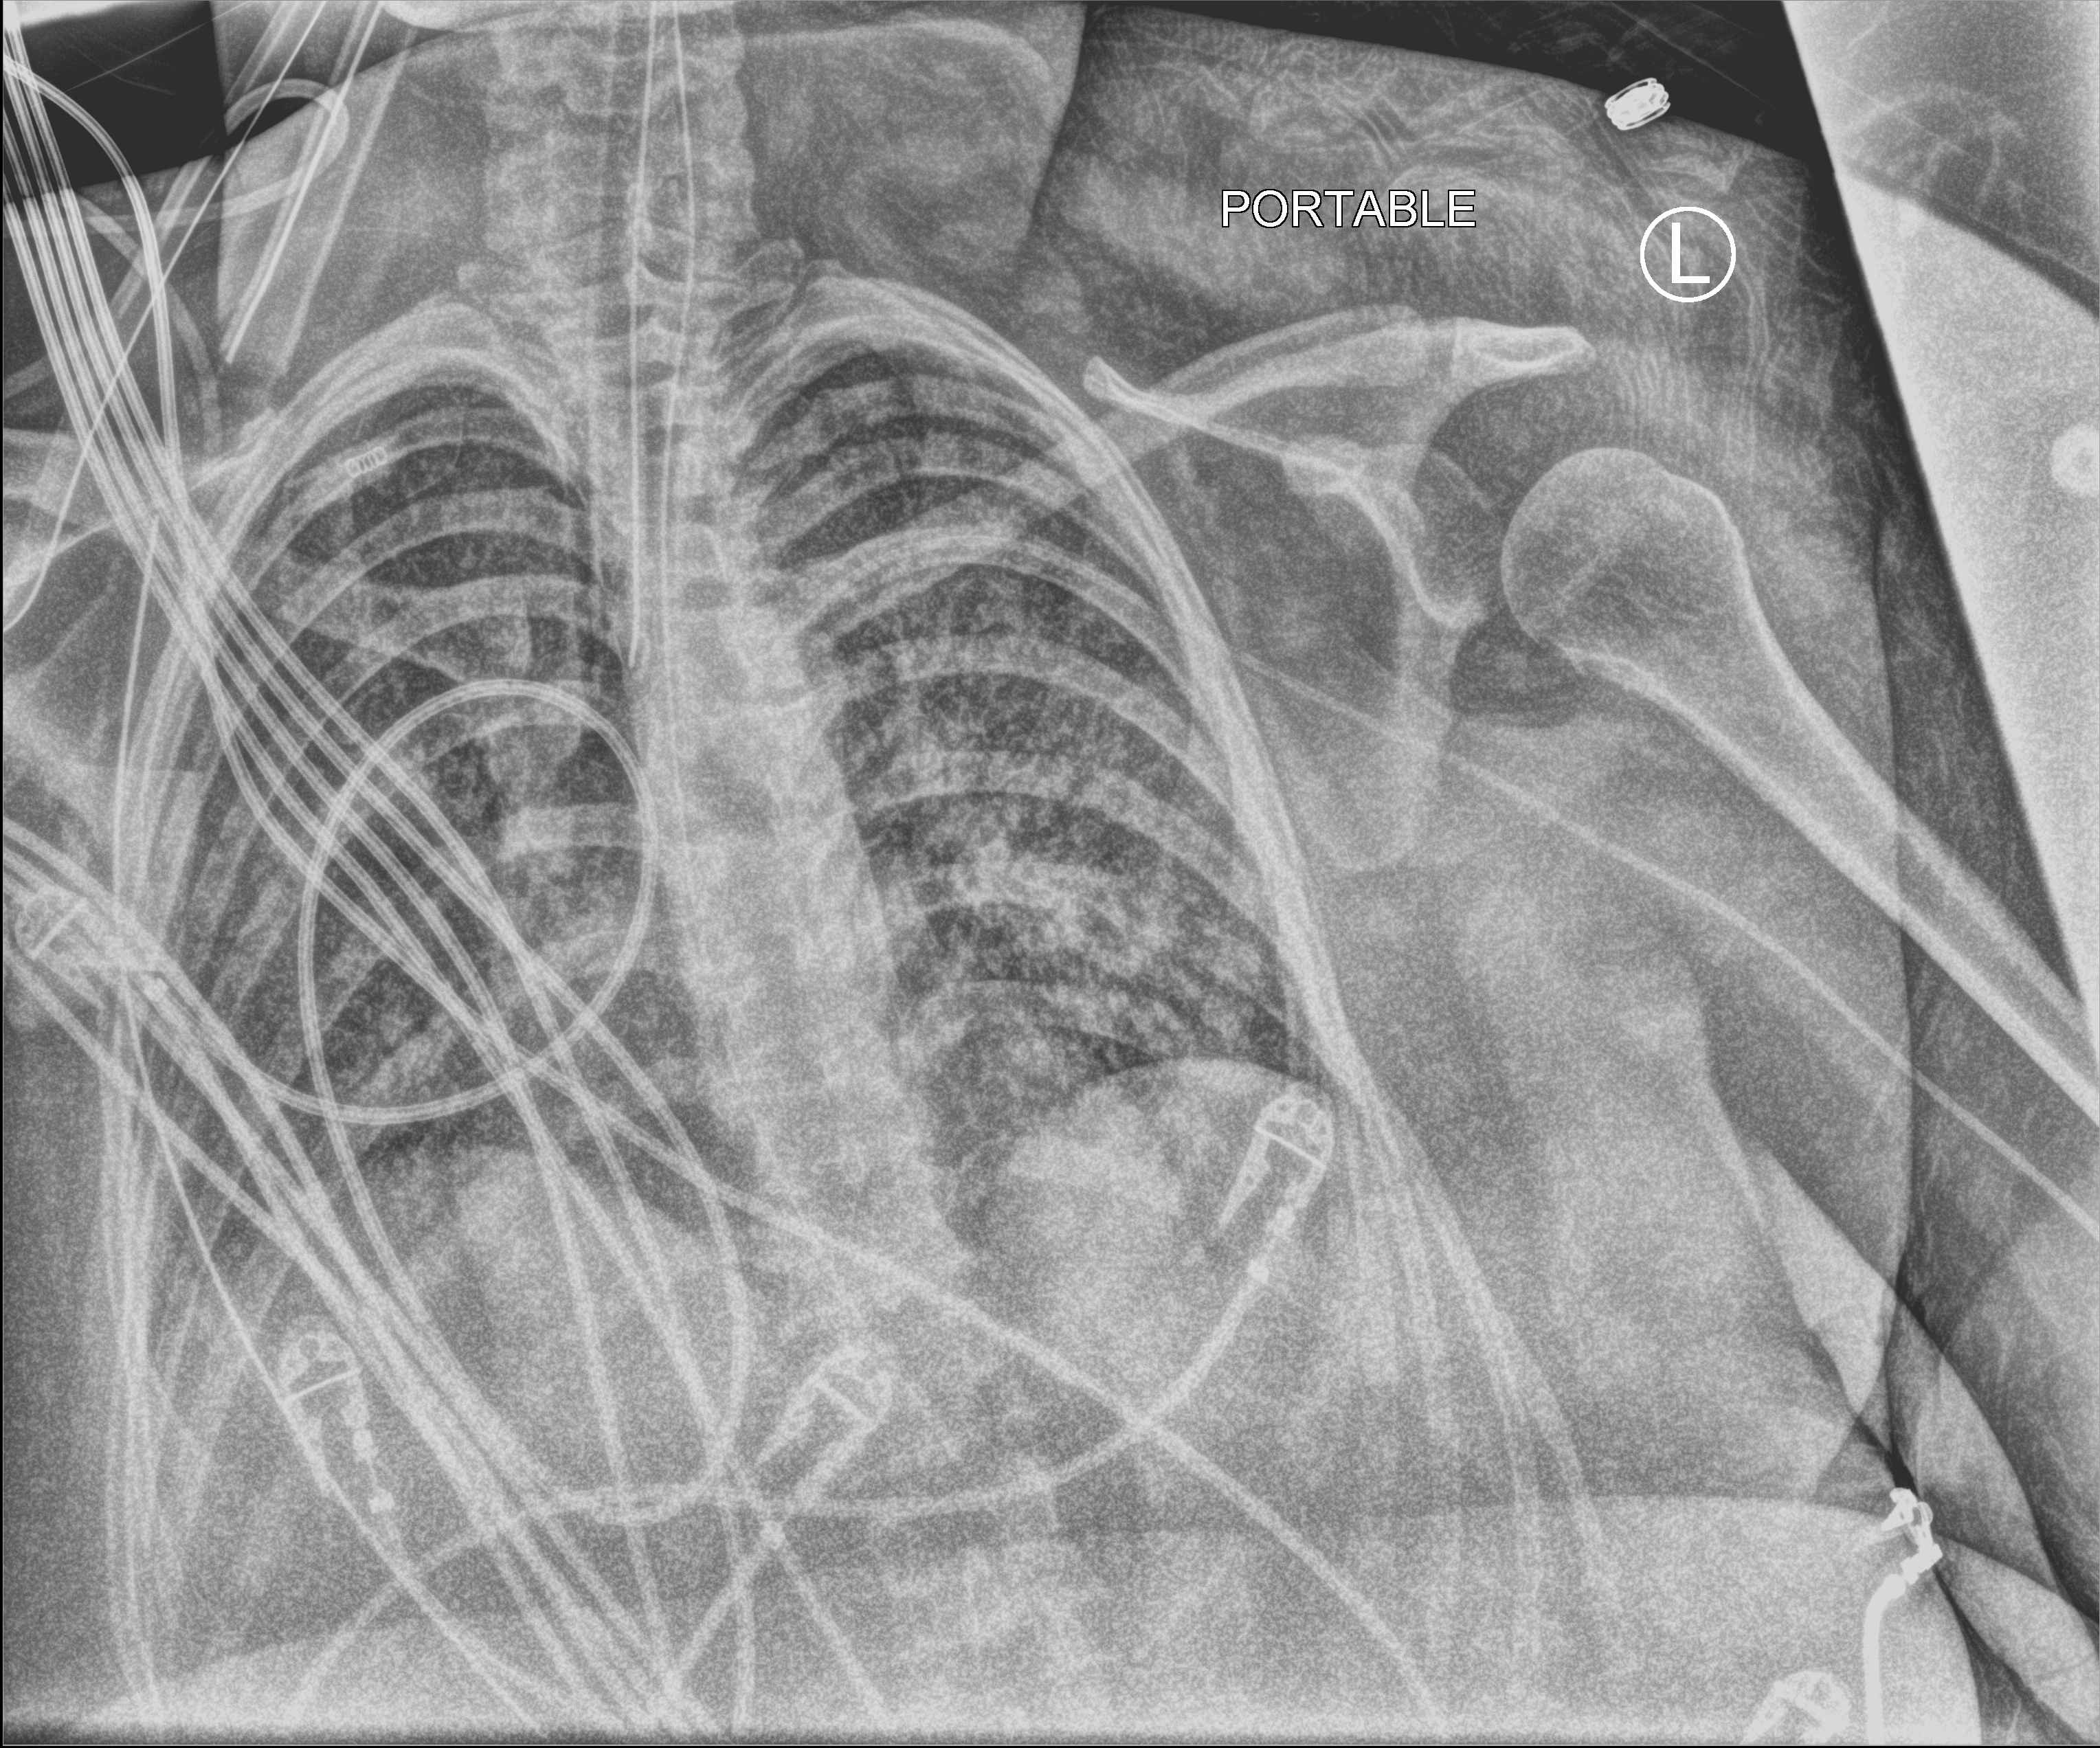
Portable chest radiograph; anteroposterior (AP) projection. Female patient hospitalised with COVID-19, age 18–59 years.
From the hospital-stay record, not from the radiograph (when in the stay this image was taken is not recorded):
- length of hospital stay: 95 days